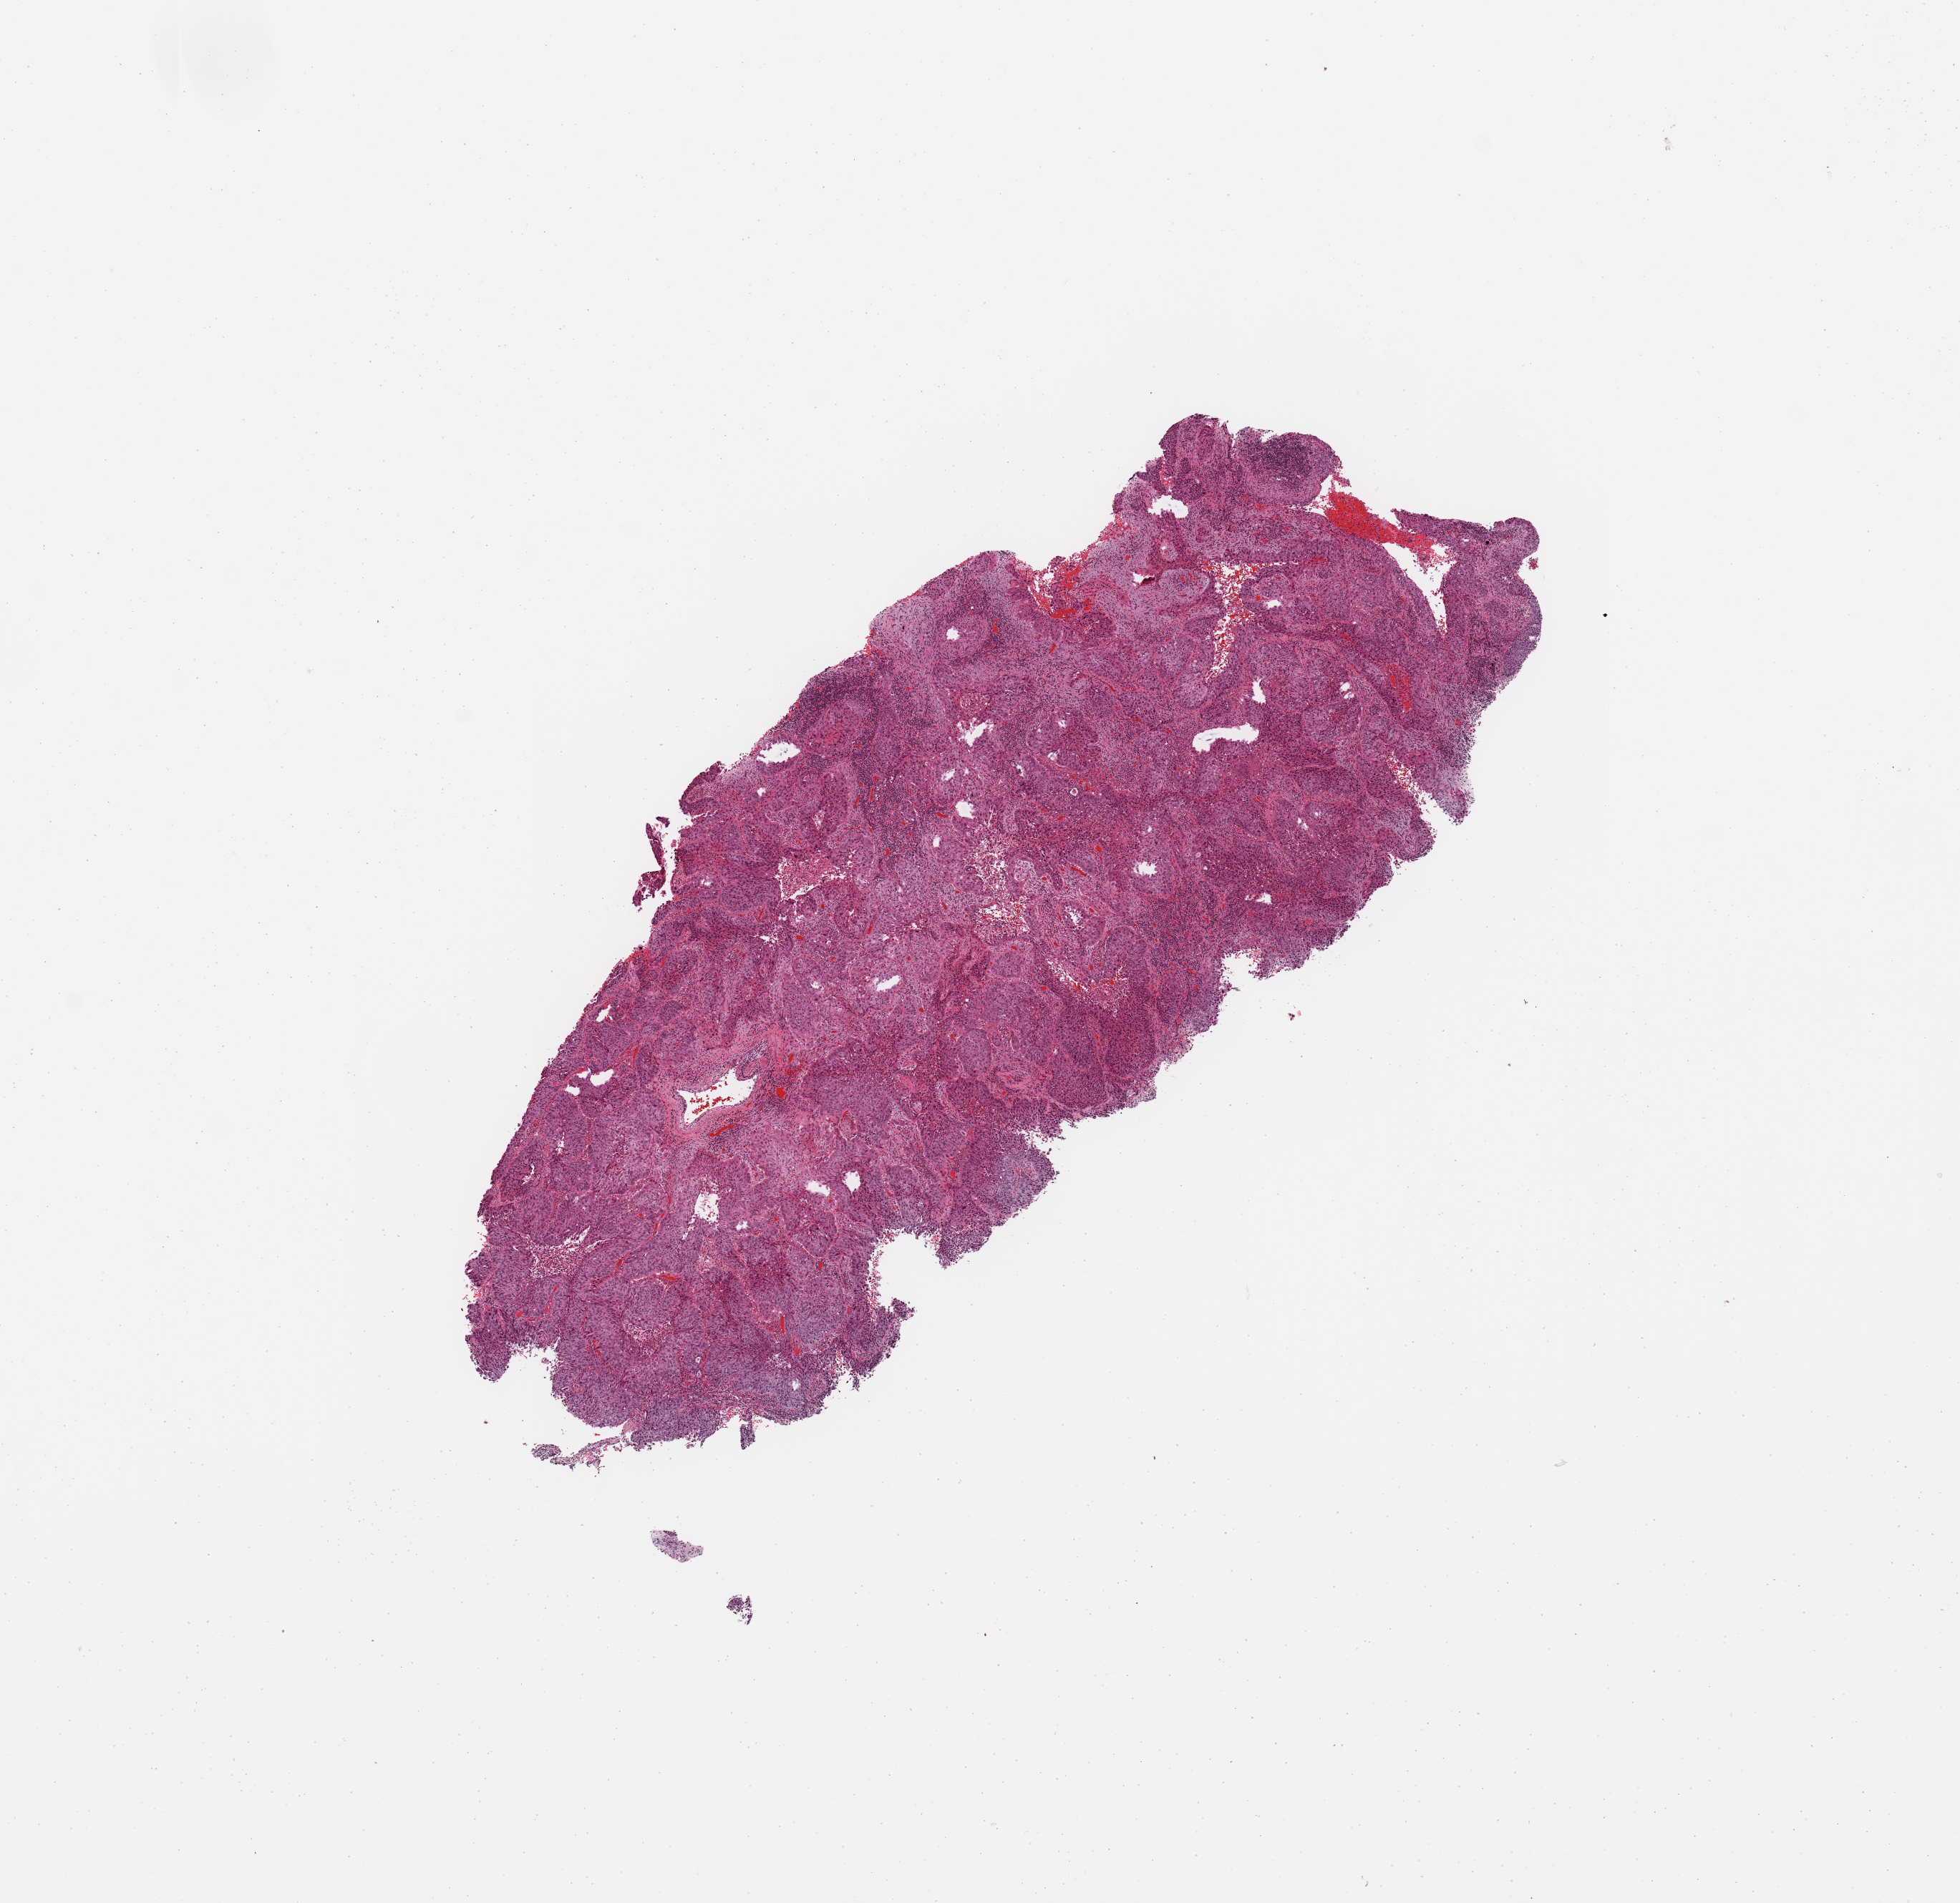
Digitized H&E tissue section (whole slide), shown as a low-resolution overview of the whole scanned area (about 10.8 x 10.5 mm); tumour tissue sample, sampled site: lung. Patient: male, age 74 years. Composition of this section per pathologist review: tumour nuclei 80%, necrosis 7%.
Histologic diagnosis: Squamous cell carcinoma, NOS.